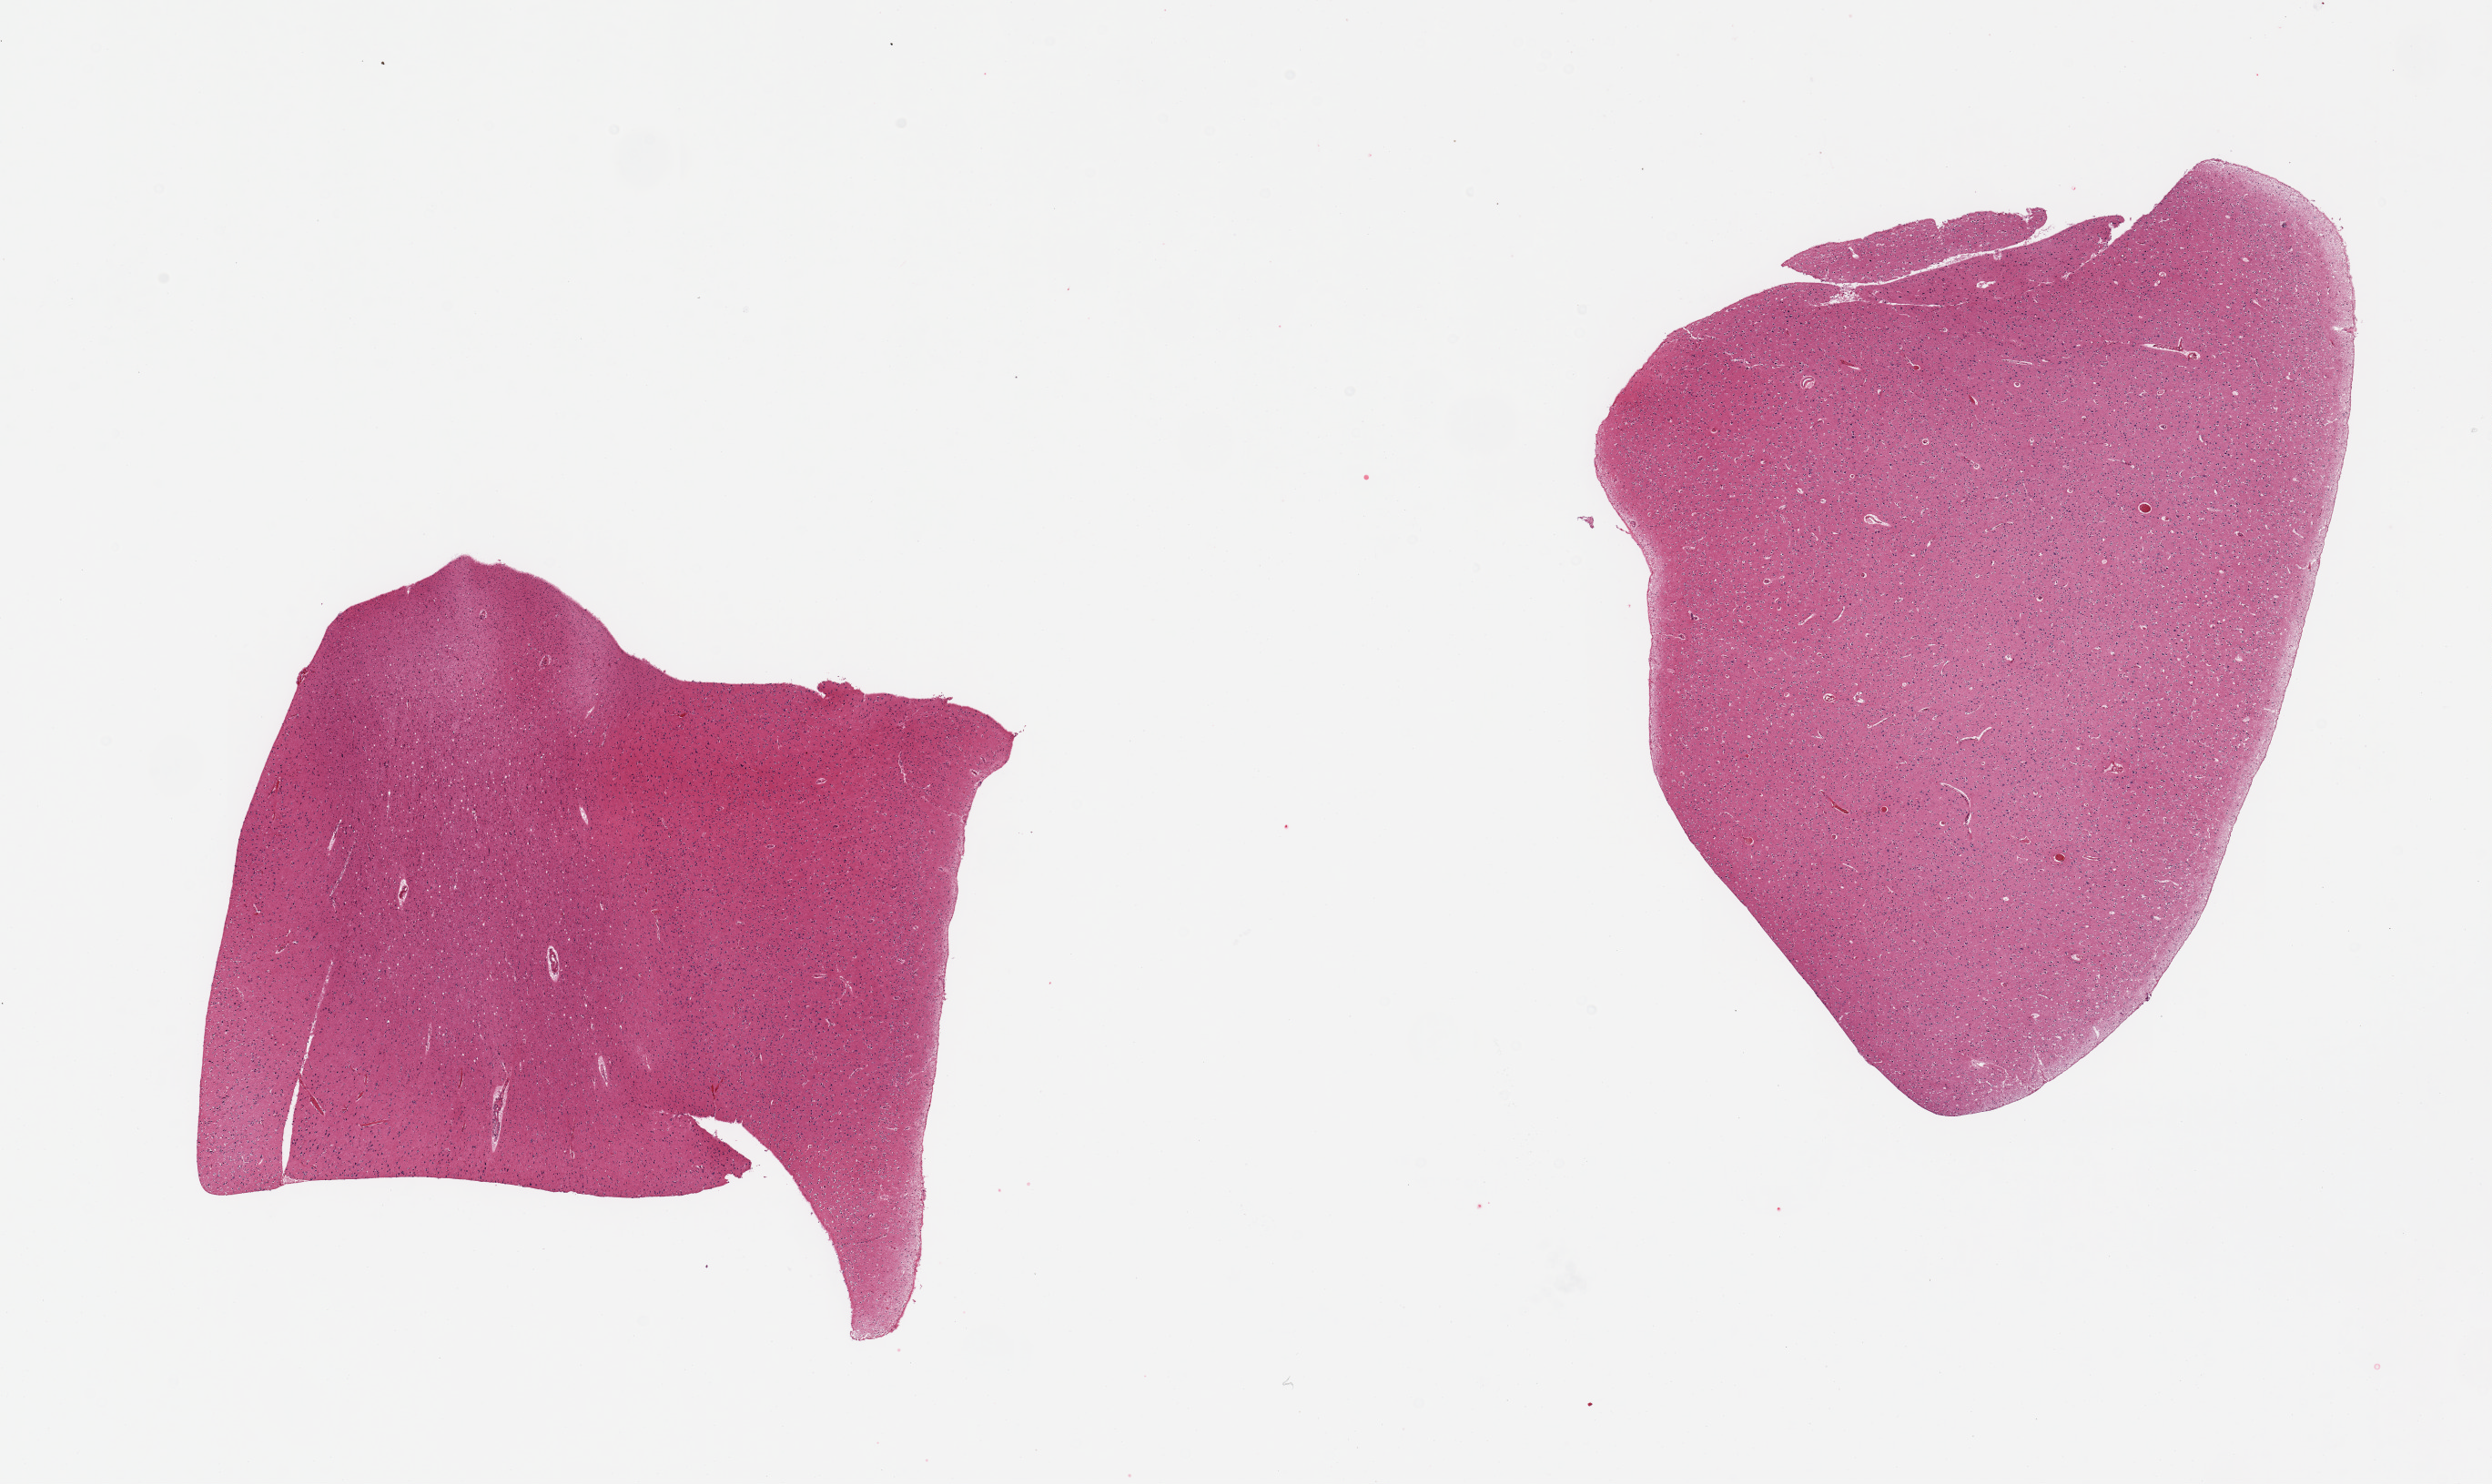
Whole-slide image, haematoxylin and eosin stain, brightfield — a low-resolution overview of the entire scanned area, about 21.7 x 12.9 mm (from a 20x scan), PAXgene-fixed, paraffin-embedded tissue, section of cerebral cortex (target tissue), tissue donor sample.
Reviewer comment on this tissue sample: 2 pieces, not the requested 4.